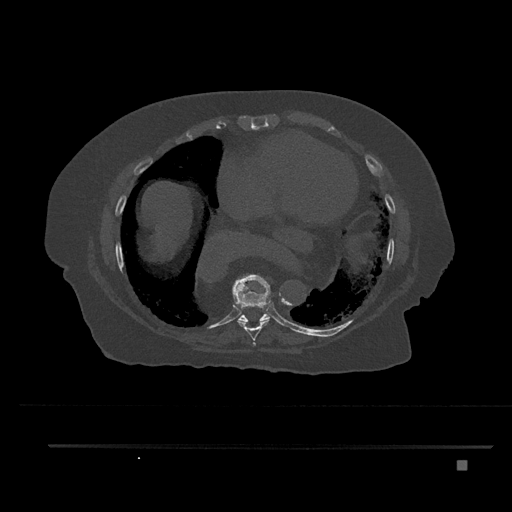
CT including the spine, one axial slice; position 425 of 797 along the scan axis; bone window (W 1800 / L 400 HU); 0.5 mm slice thickness; 512 × 512 image matrix. Patient: female, 76 years. Case-level facts recorded for this patient, not image findings: primary cancer: lung.
Structures marked on this image (semi-automatic segmentation, software-assisted and operator-edited):
- T8 vertebra: bounding box [x1, y1, x2, y2] px = [233, 274, 271, 346]
- T9 vertebra: [238, 286, 271, 322]